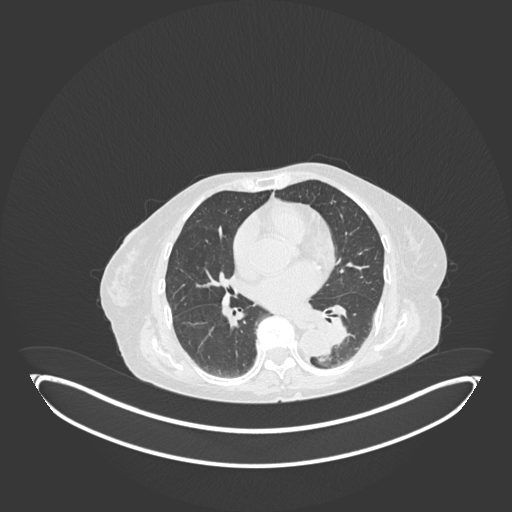
Chest CT, one axial slice; slice 54 of 189 in the series (ordered by position); 120 kVp; lung window (W 1500 / L -600 HU); 512 × 512 image matrix, field of view 500 × 500 mm. Female patient, age 82 years. From the clinical record (not read from this slice): clinical TNM (as recorded): T1b N0 M1.
Outlined on this slice (rectangle marked by the reading radiologist):
- lung tumour (recorded histology: adenocarcinoma): bounding box [x1, y1, x2, y2] px = [313, 314, 354, 354]